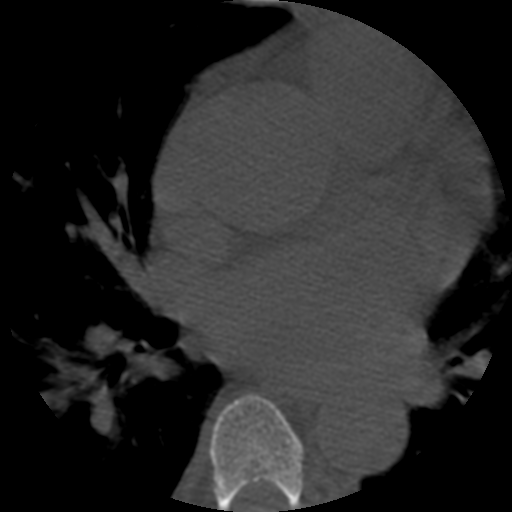
CT including the spine, one axial slice. Position 354 of 508 along the scan axis. Reconstruction kernel STANDARD. Bone window (W 1800 / L 400 HU). 1.25 mm slice thickness. 512 × 512 image matrix, field of view 160 × 160 mm. Patient age 57 years. From the clinical record (not read from this slice): primary cancer: prostate.
Outlined on this slice (semi-automatically segmented with operator editing):
- T6 vertebra: bounding box <209,395,304,512> (left, top, right, bottom; pixels)